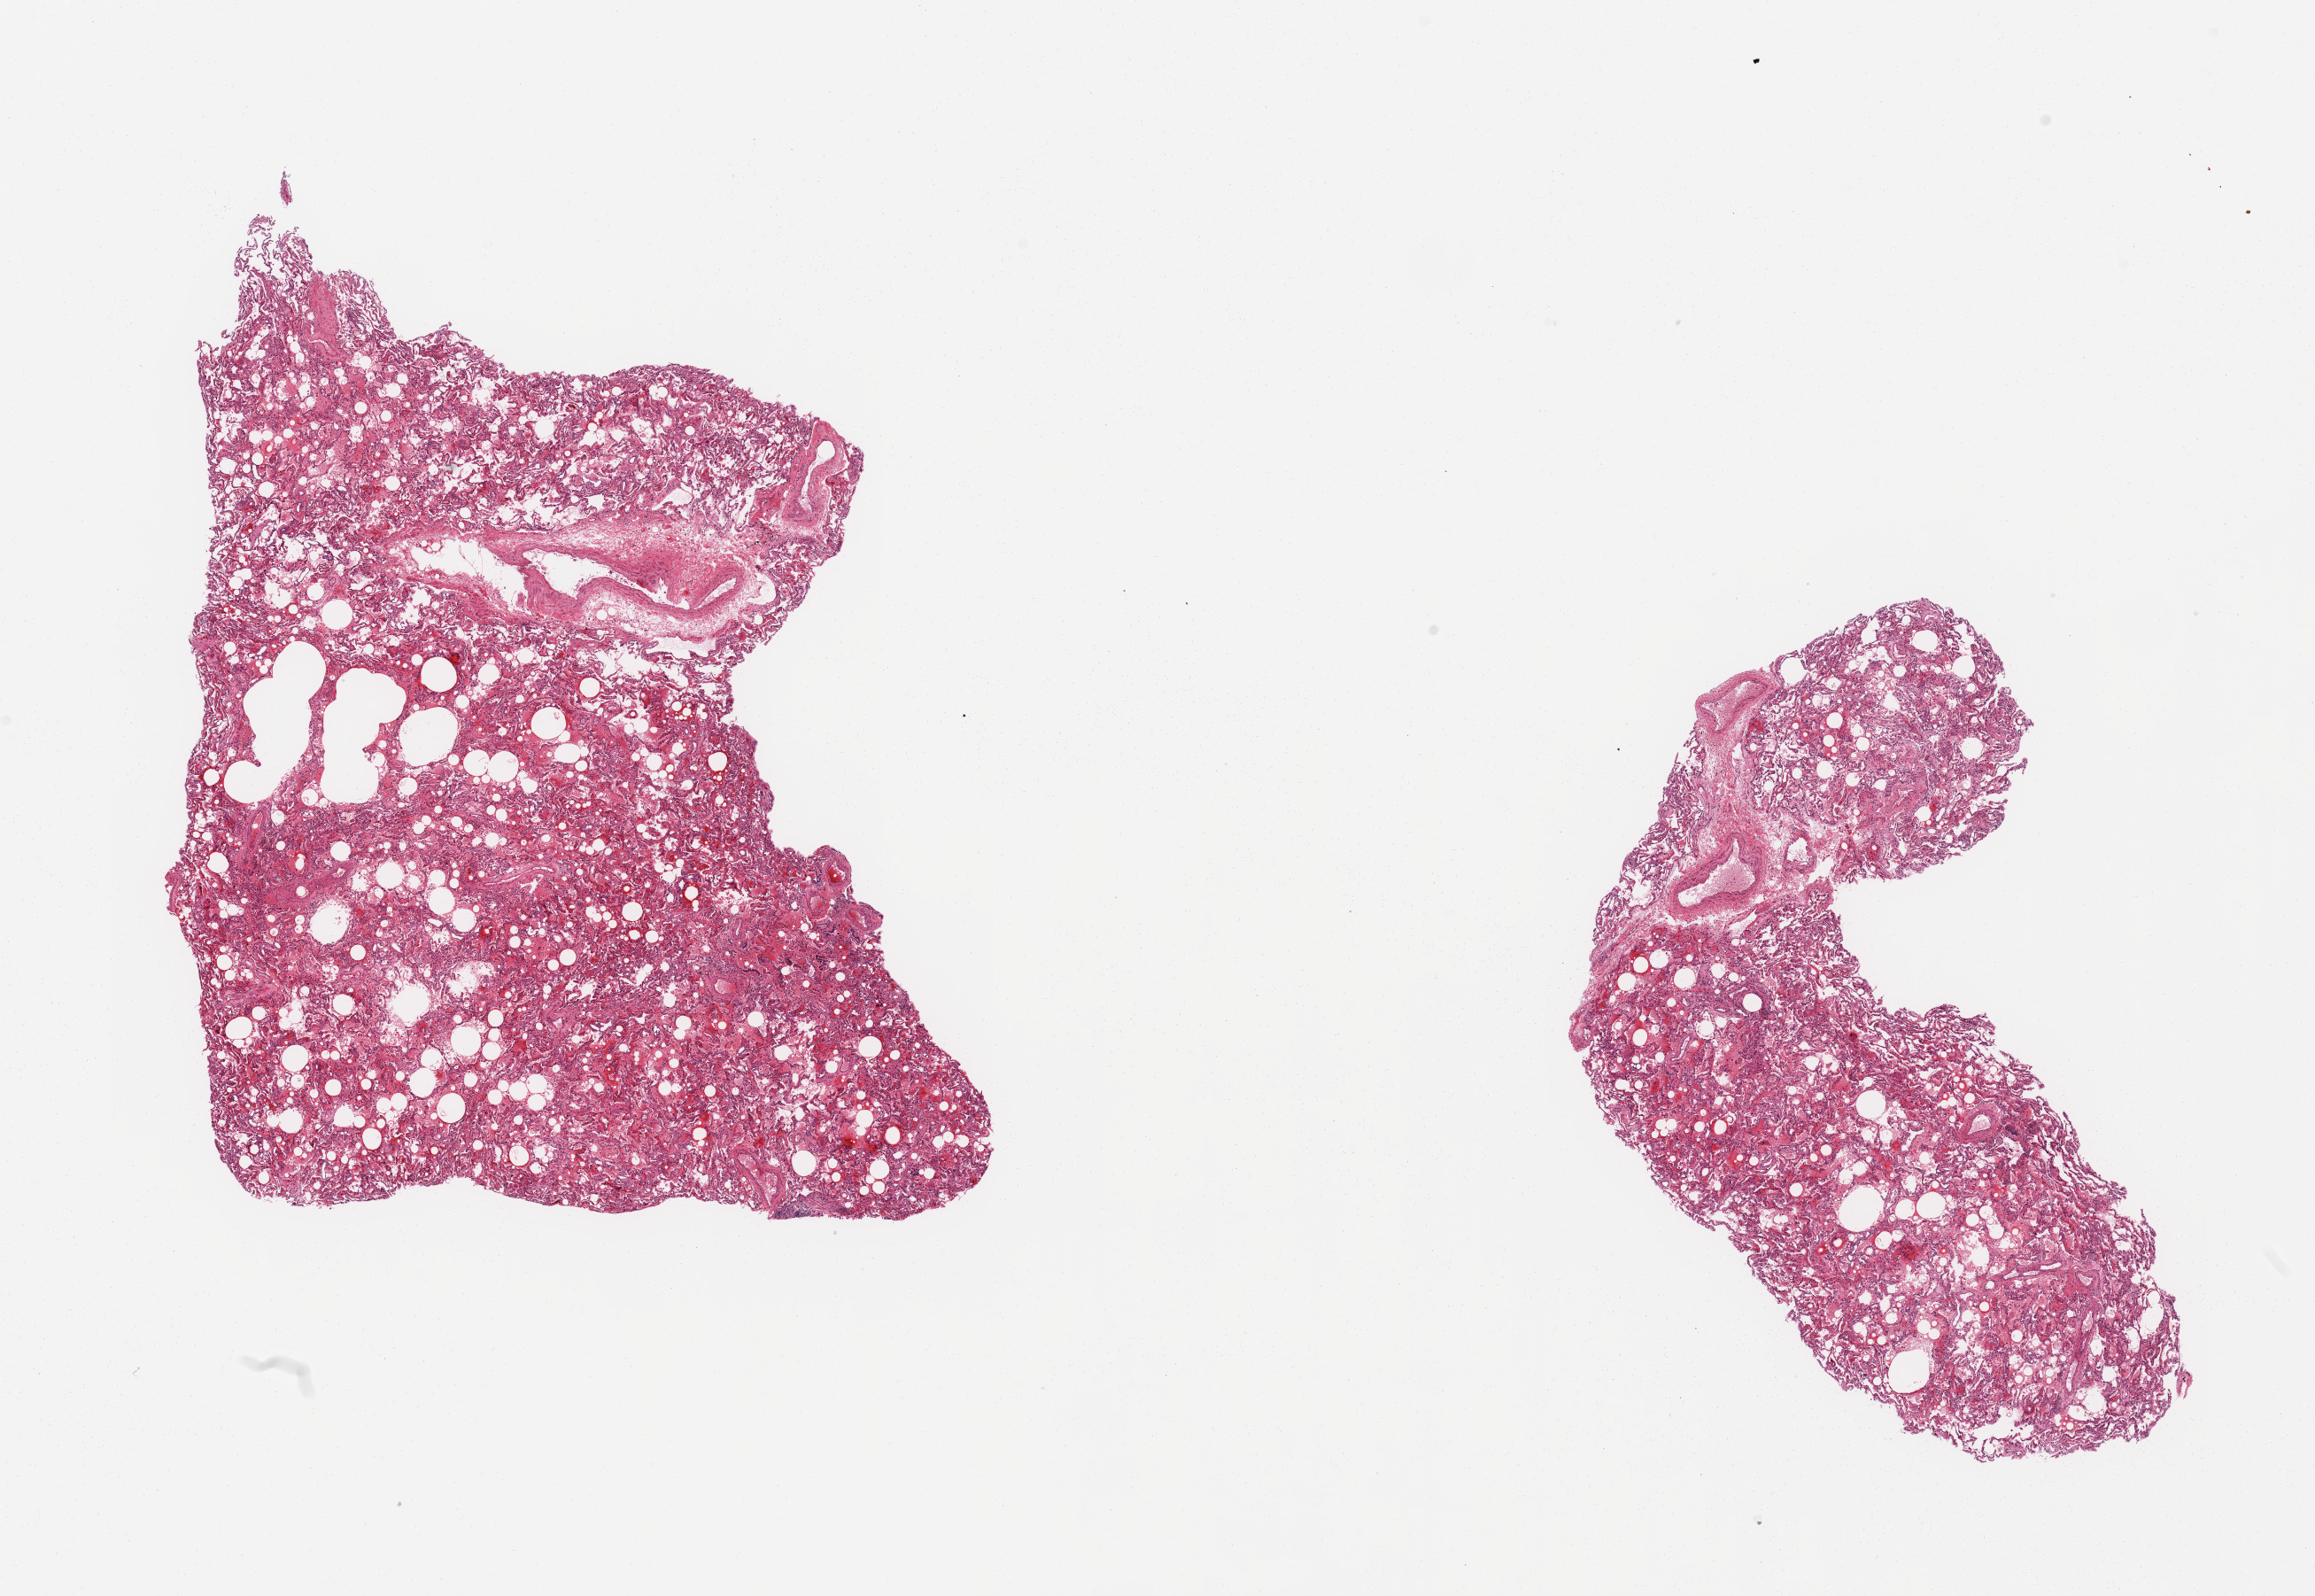
Haematoxylin and eosin whole-slide image, a low-resolution overview of the entire scanned area, about 20.7 x 14.3 mm; PAXgene-fixed paraffin-embedded (PFPE) section; sampled site (target tissue): lung; tissue donor sample. Donor sex: male.
Pathologist's review note for this sample: 2 pieces; moderate vascular congestion and alveolar hemorrhage.